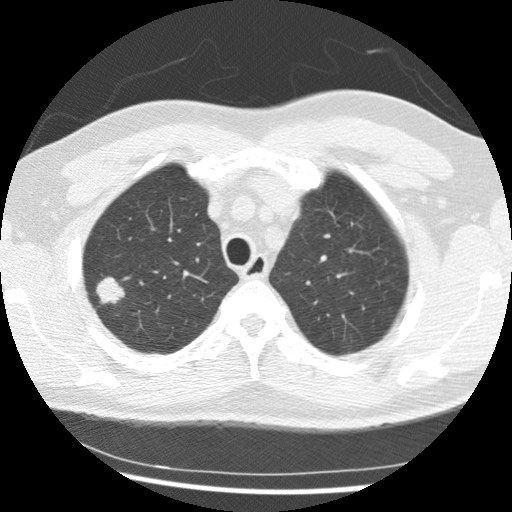
Low-dose screening chest CT, axial slice, baseline annual screen, lung window (W 1500 / L -600 HU), standard (soft-tissue) reconstruction kernel (STANDARD), slice 54 of 265 in the series. Male, age 56 years at enrolment. Current smoker at enrolment.
Expert reader's lesion annotation, bounding box <81,271,132,315> (left, top, right, bottom; pixels). Reader record for this screening exam (exam-level; its link to the box is not recorded): non-calcified nodule or mass ≥4 mm, right upper lobe, 19 × 15 mm, spiculated (stellate) margins, soft tissue attenuation.